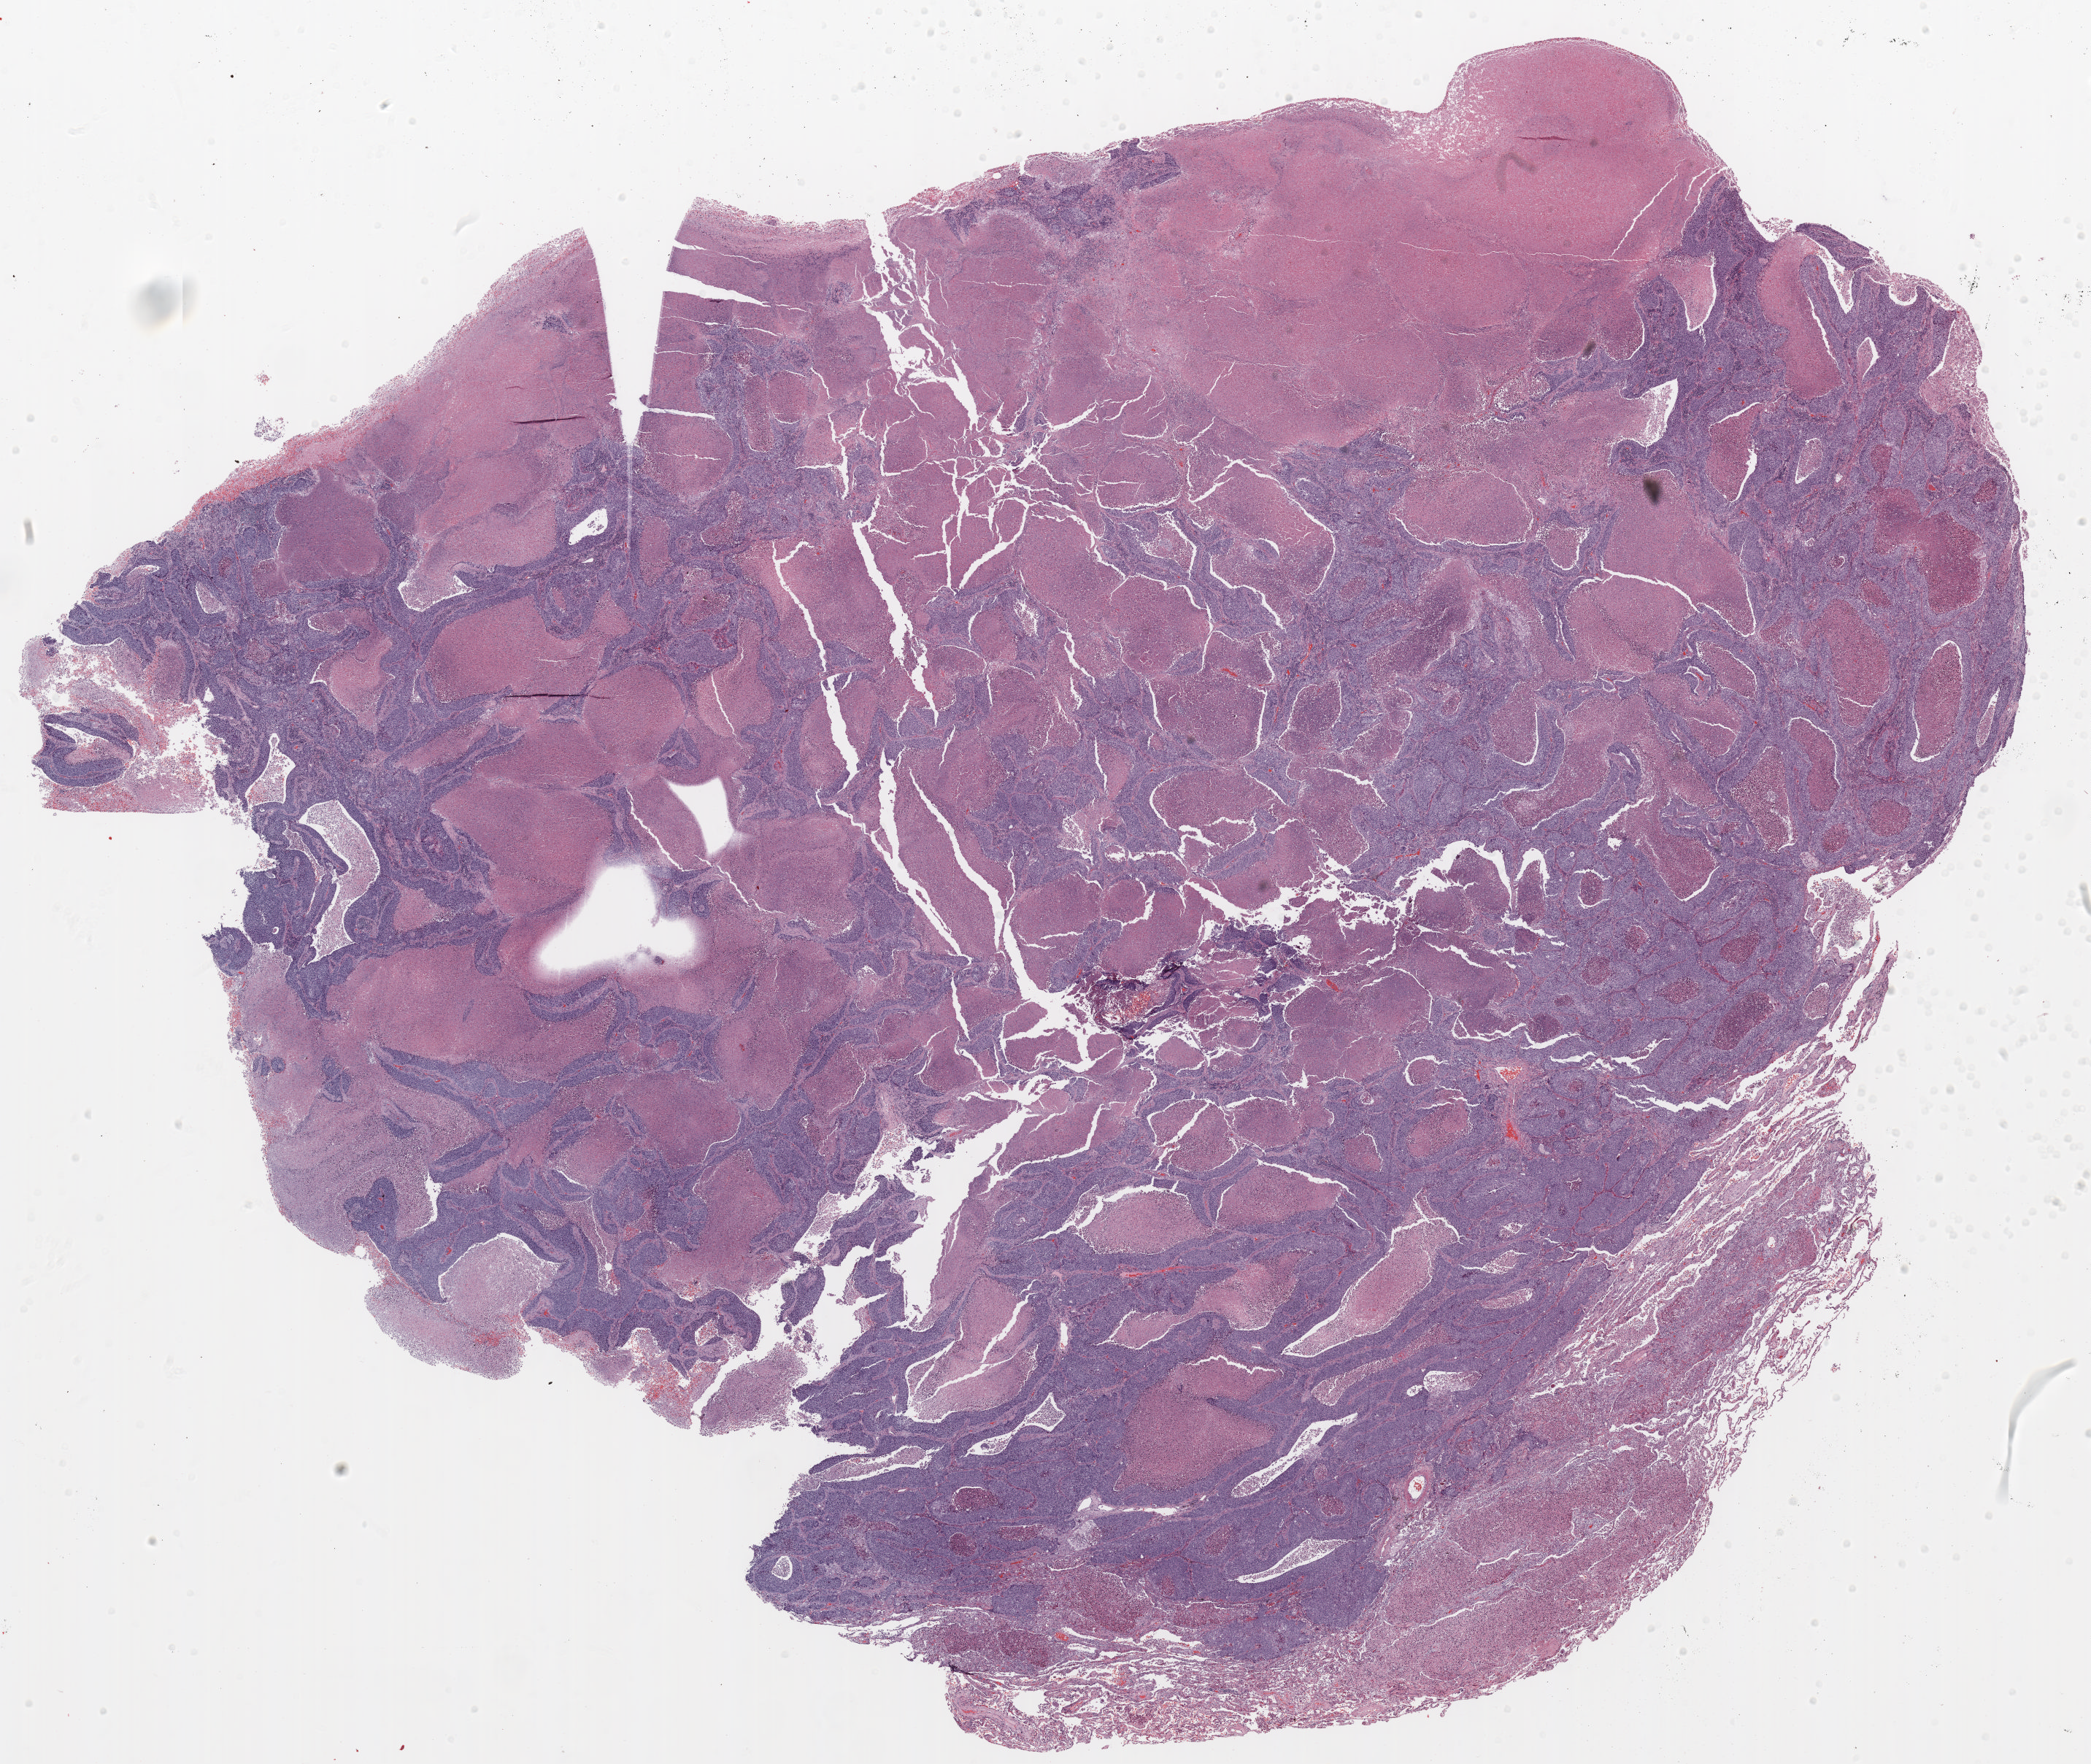
H&E whole-slide image — shown as a low-resolution overview of the whole scanned area (about 23.0 x 19.4 mm, slide scanned at 20x). Formalin-fixed paraffin-embedded (FFPE) section. Lung. Male patient, aged 72 at enrolment. Current smoker at enrolment. Grade: poorly differentiated (G3).
• tumour size (pathology): 100 mm
• primary tumour location (clinical record): left lower lobe
• participant's lung-cancer diagnosis: Large cell carcinoma, NOS
• stage (AJCC 6th edition): IB